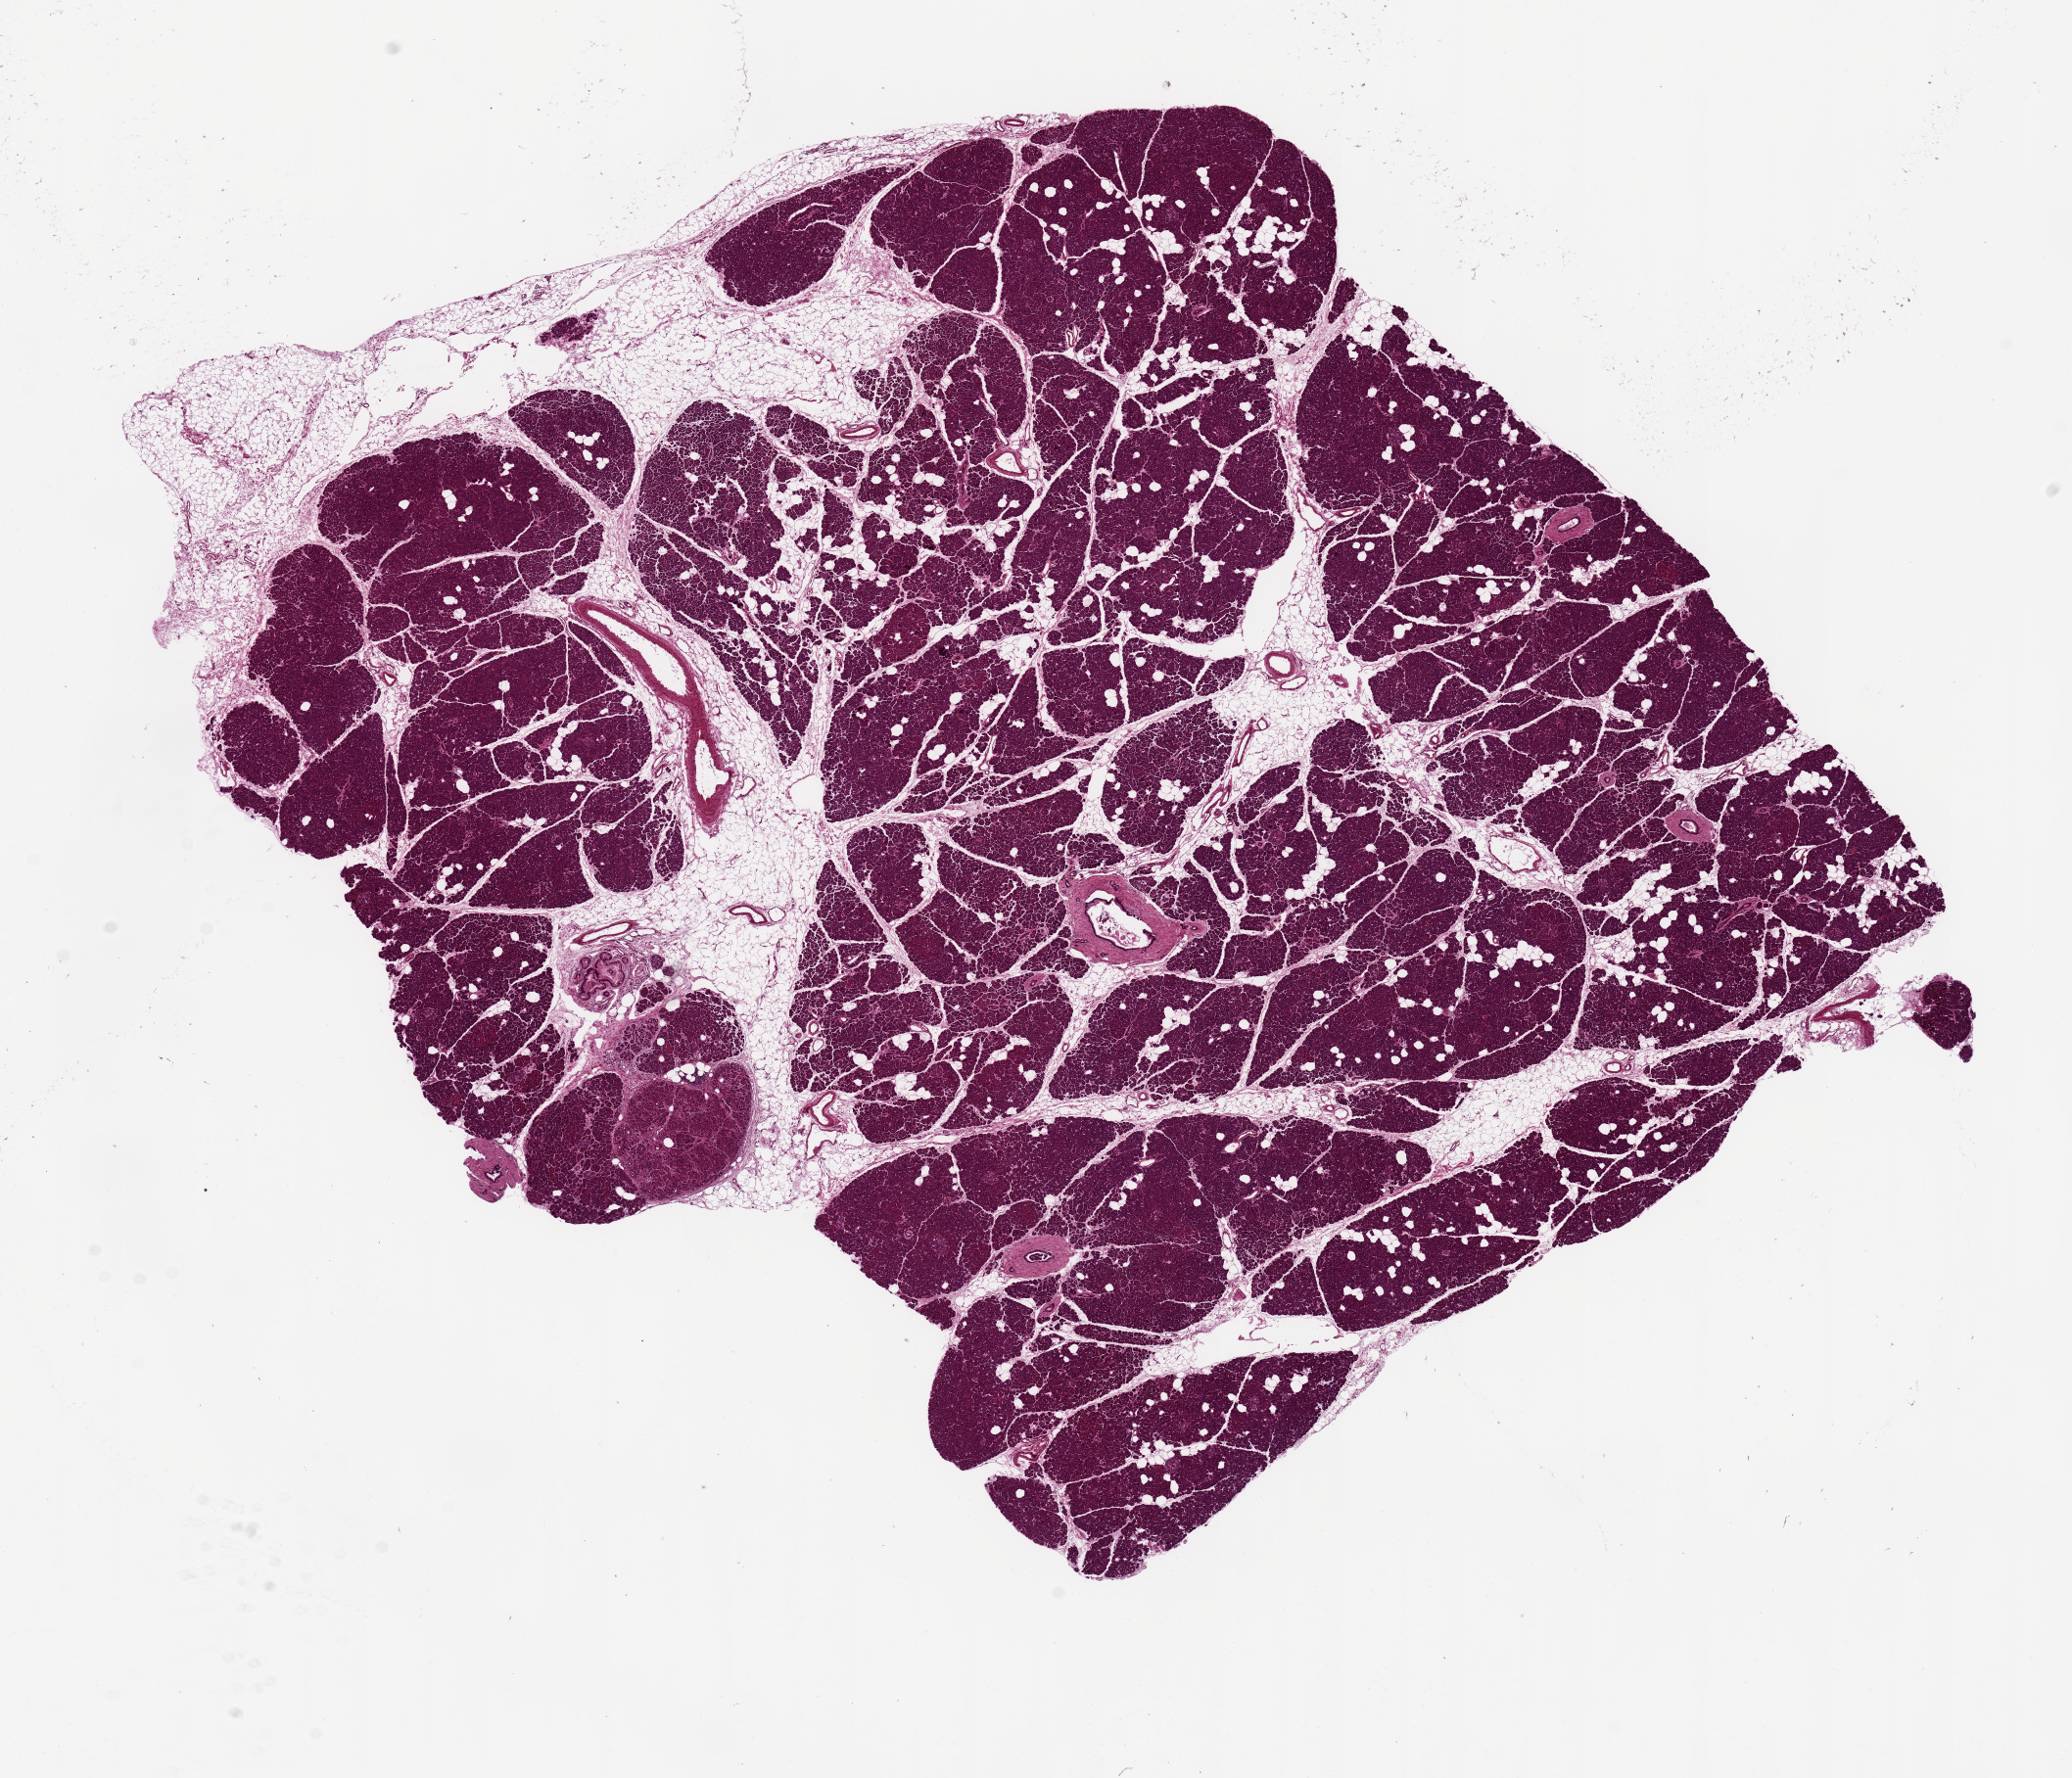
Digitized haematoxylin and eosin-stained section — shown as a low-resolution overview of the whole scanned area (about 16.7 x 14.4 mm, acquisition: 20x scan). PAXgene-fixed paraffin-embedded (PFPE) section. Sampled site (target tissue): pancreas. Donor tissue sample. Donor sex: female.
* reviewer comment on this tissue sample: ~9x9mm, well fixed, about 20% intermingled fat